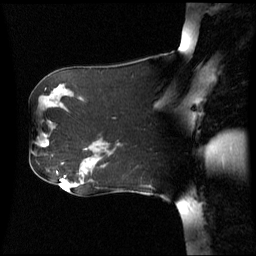
Breast MRI (dynamic contrast-enhanced), one sagittal slice; position 36 of 60 along the scan axis; dynamic contrast-enhanced series, image 2 of 3 at this slice position (ordered by acquisition); 1.5 T; TE 4.2 ms, TR 8.4 ms; 2.5 mm slice thickness; 256 × 256 image matrix, field of view 260 × 260 mm. Female patient, age 62 years. From the clinical record (not read from this slice): setting: breast cancer imaged before/during neoadjuvant chemotherapy; receptor status: HR-positive, HER2-negative.
Structures marked on this image (semi-automatically segmented with operator editing):
- analysis volume of interest (the breast-tissue region the enhancement analysis was run in; not a lesion): bounding box <30,121,58,159> (left, top, right, bottom; pixels)
- tumour enhancement mask (voxels above the 70 % enhancement threshold inside the analysis volume of interest): <43,142,50,148>